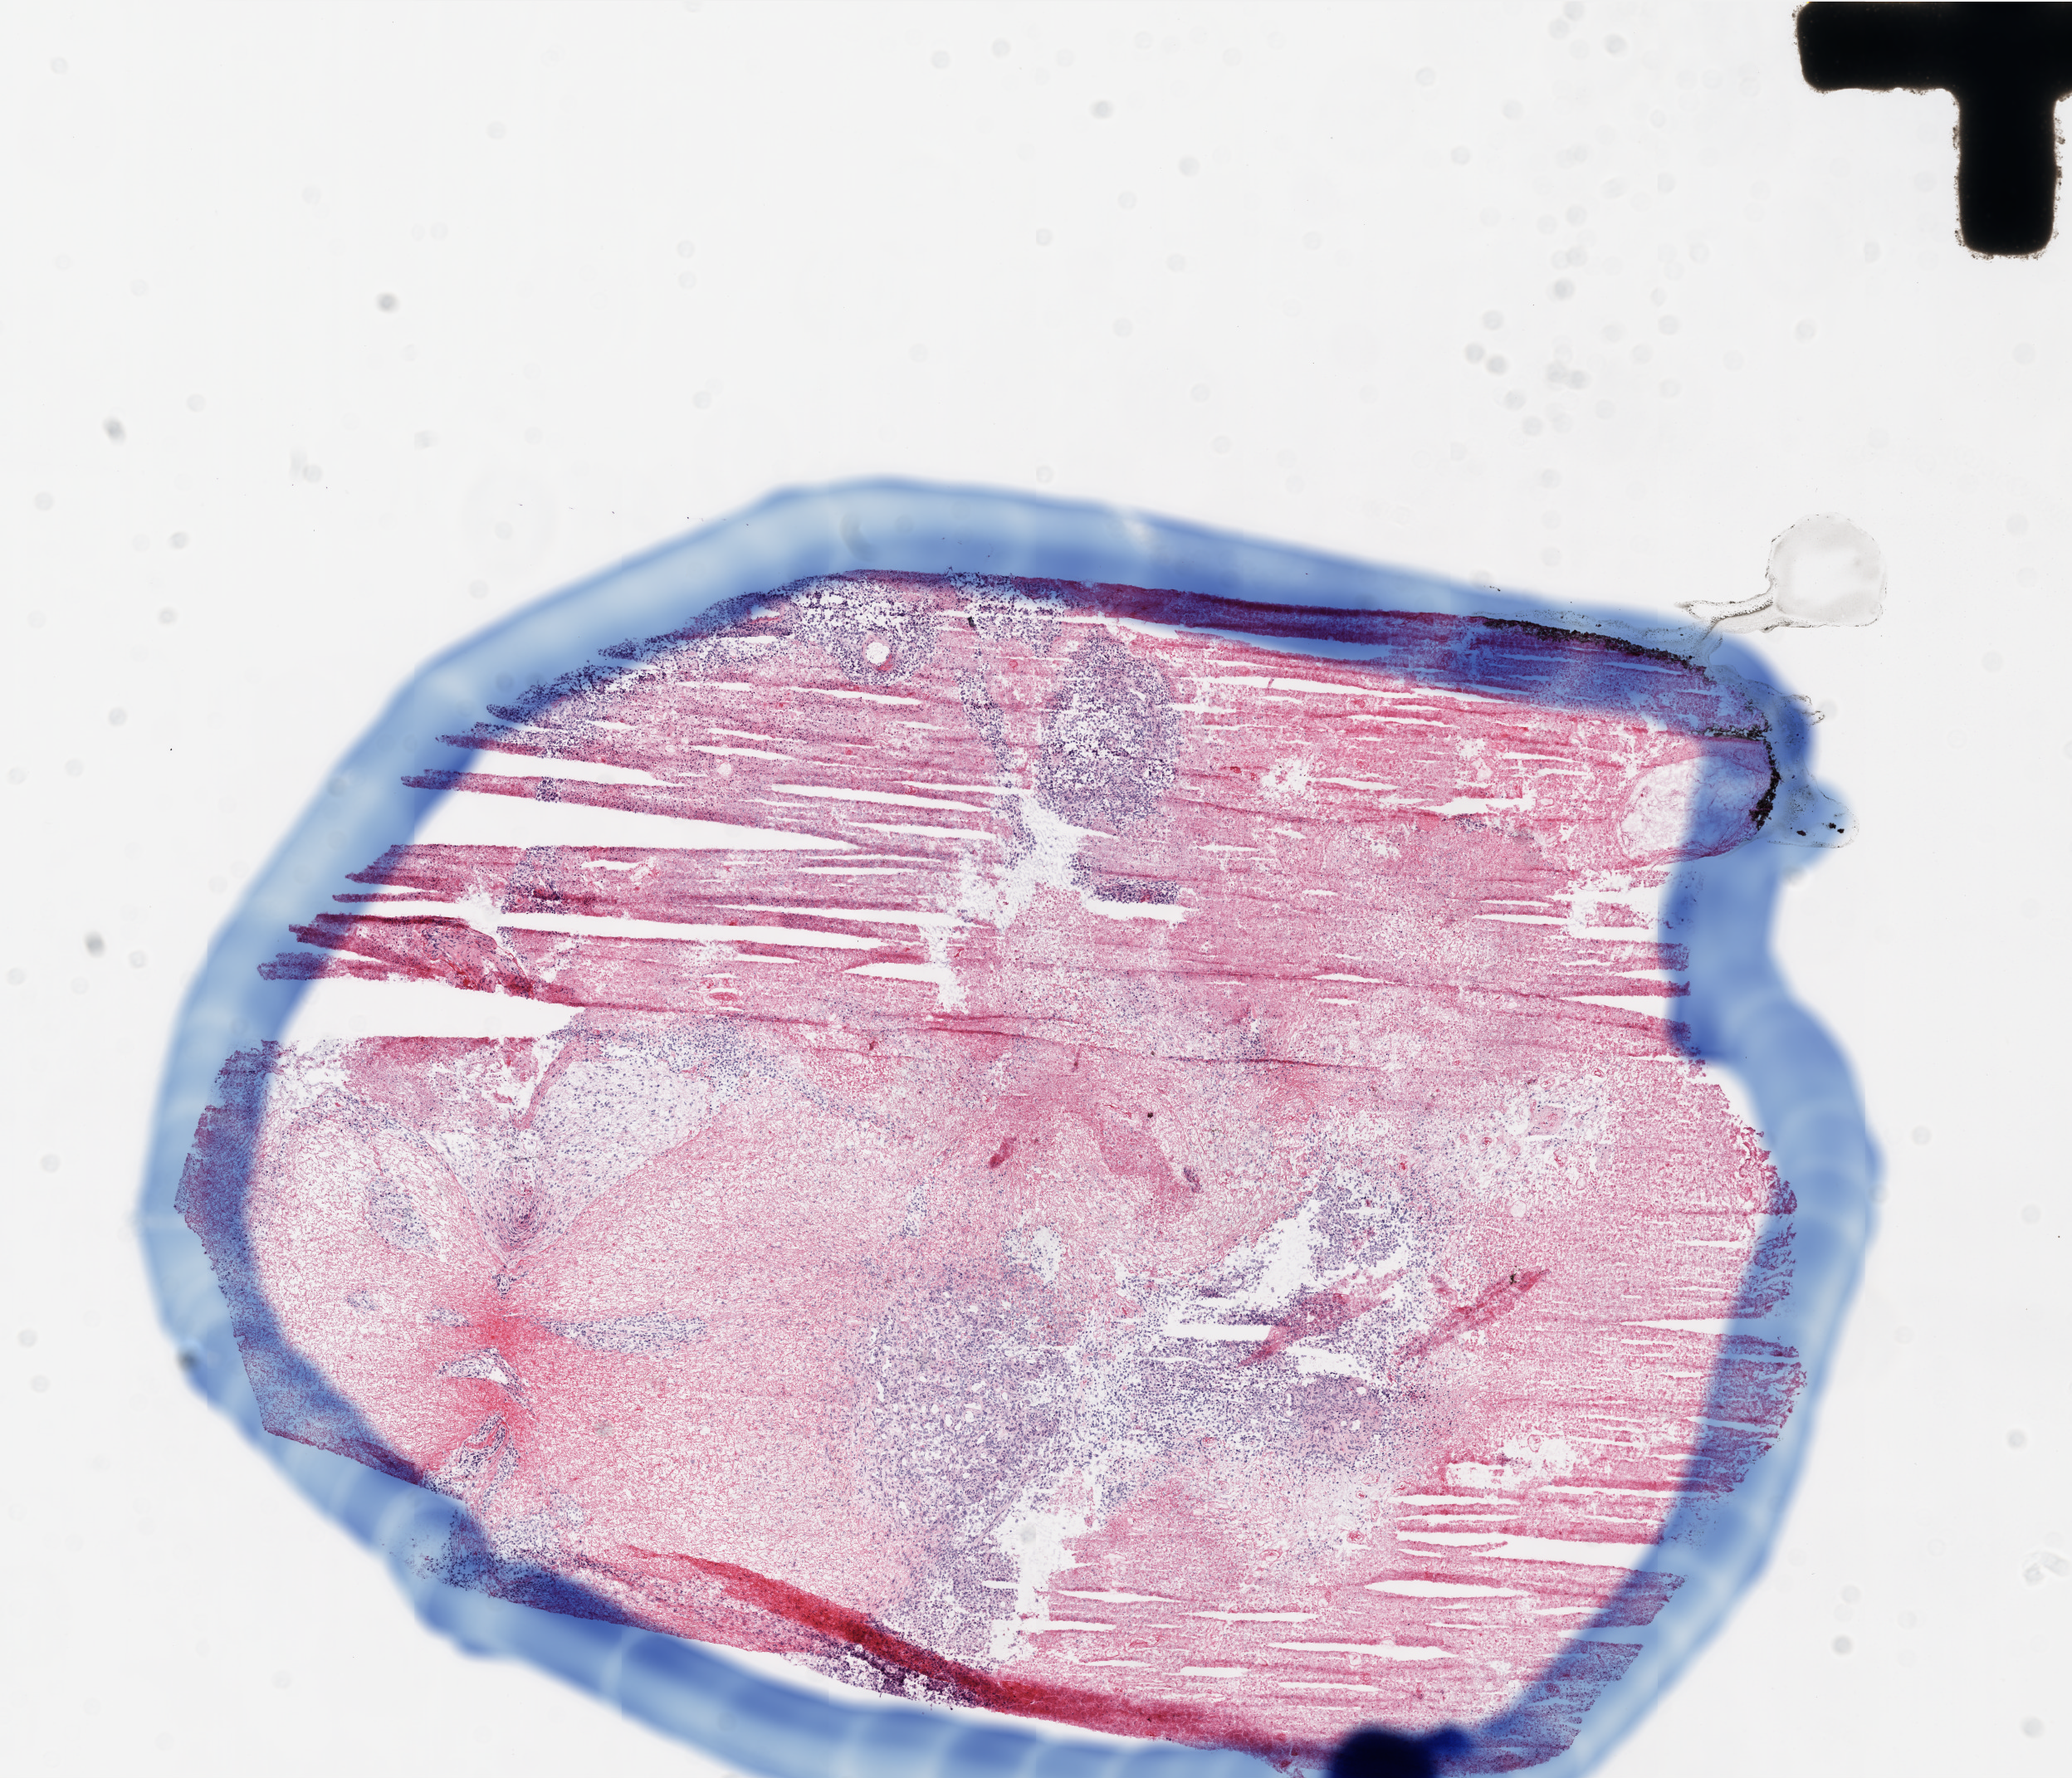
H&E whole-slide image — a low-resolution overview of the entire scanned area, about 10.0 x 8.6 mm, frozen section from the top of the tissue portion, sample: primary tumour, brain. Female, age 32 years at initial diagnosis. Pathologist review of this section (percent, as recorded): tumour cells 20%, tumour nuclei 100%, normal cells 0%, stromal cells 0%, necrosis 80%.
Diagnosis: Glioblastoma.